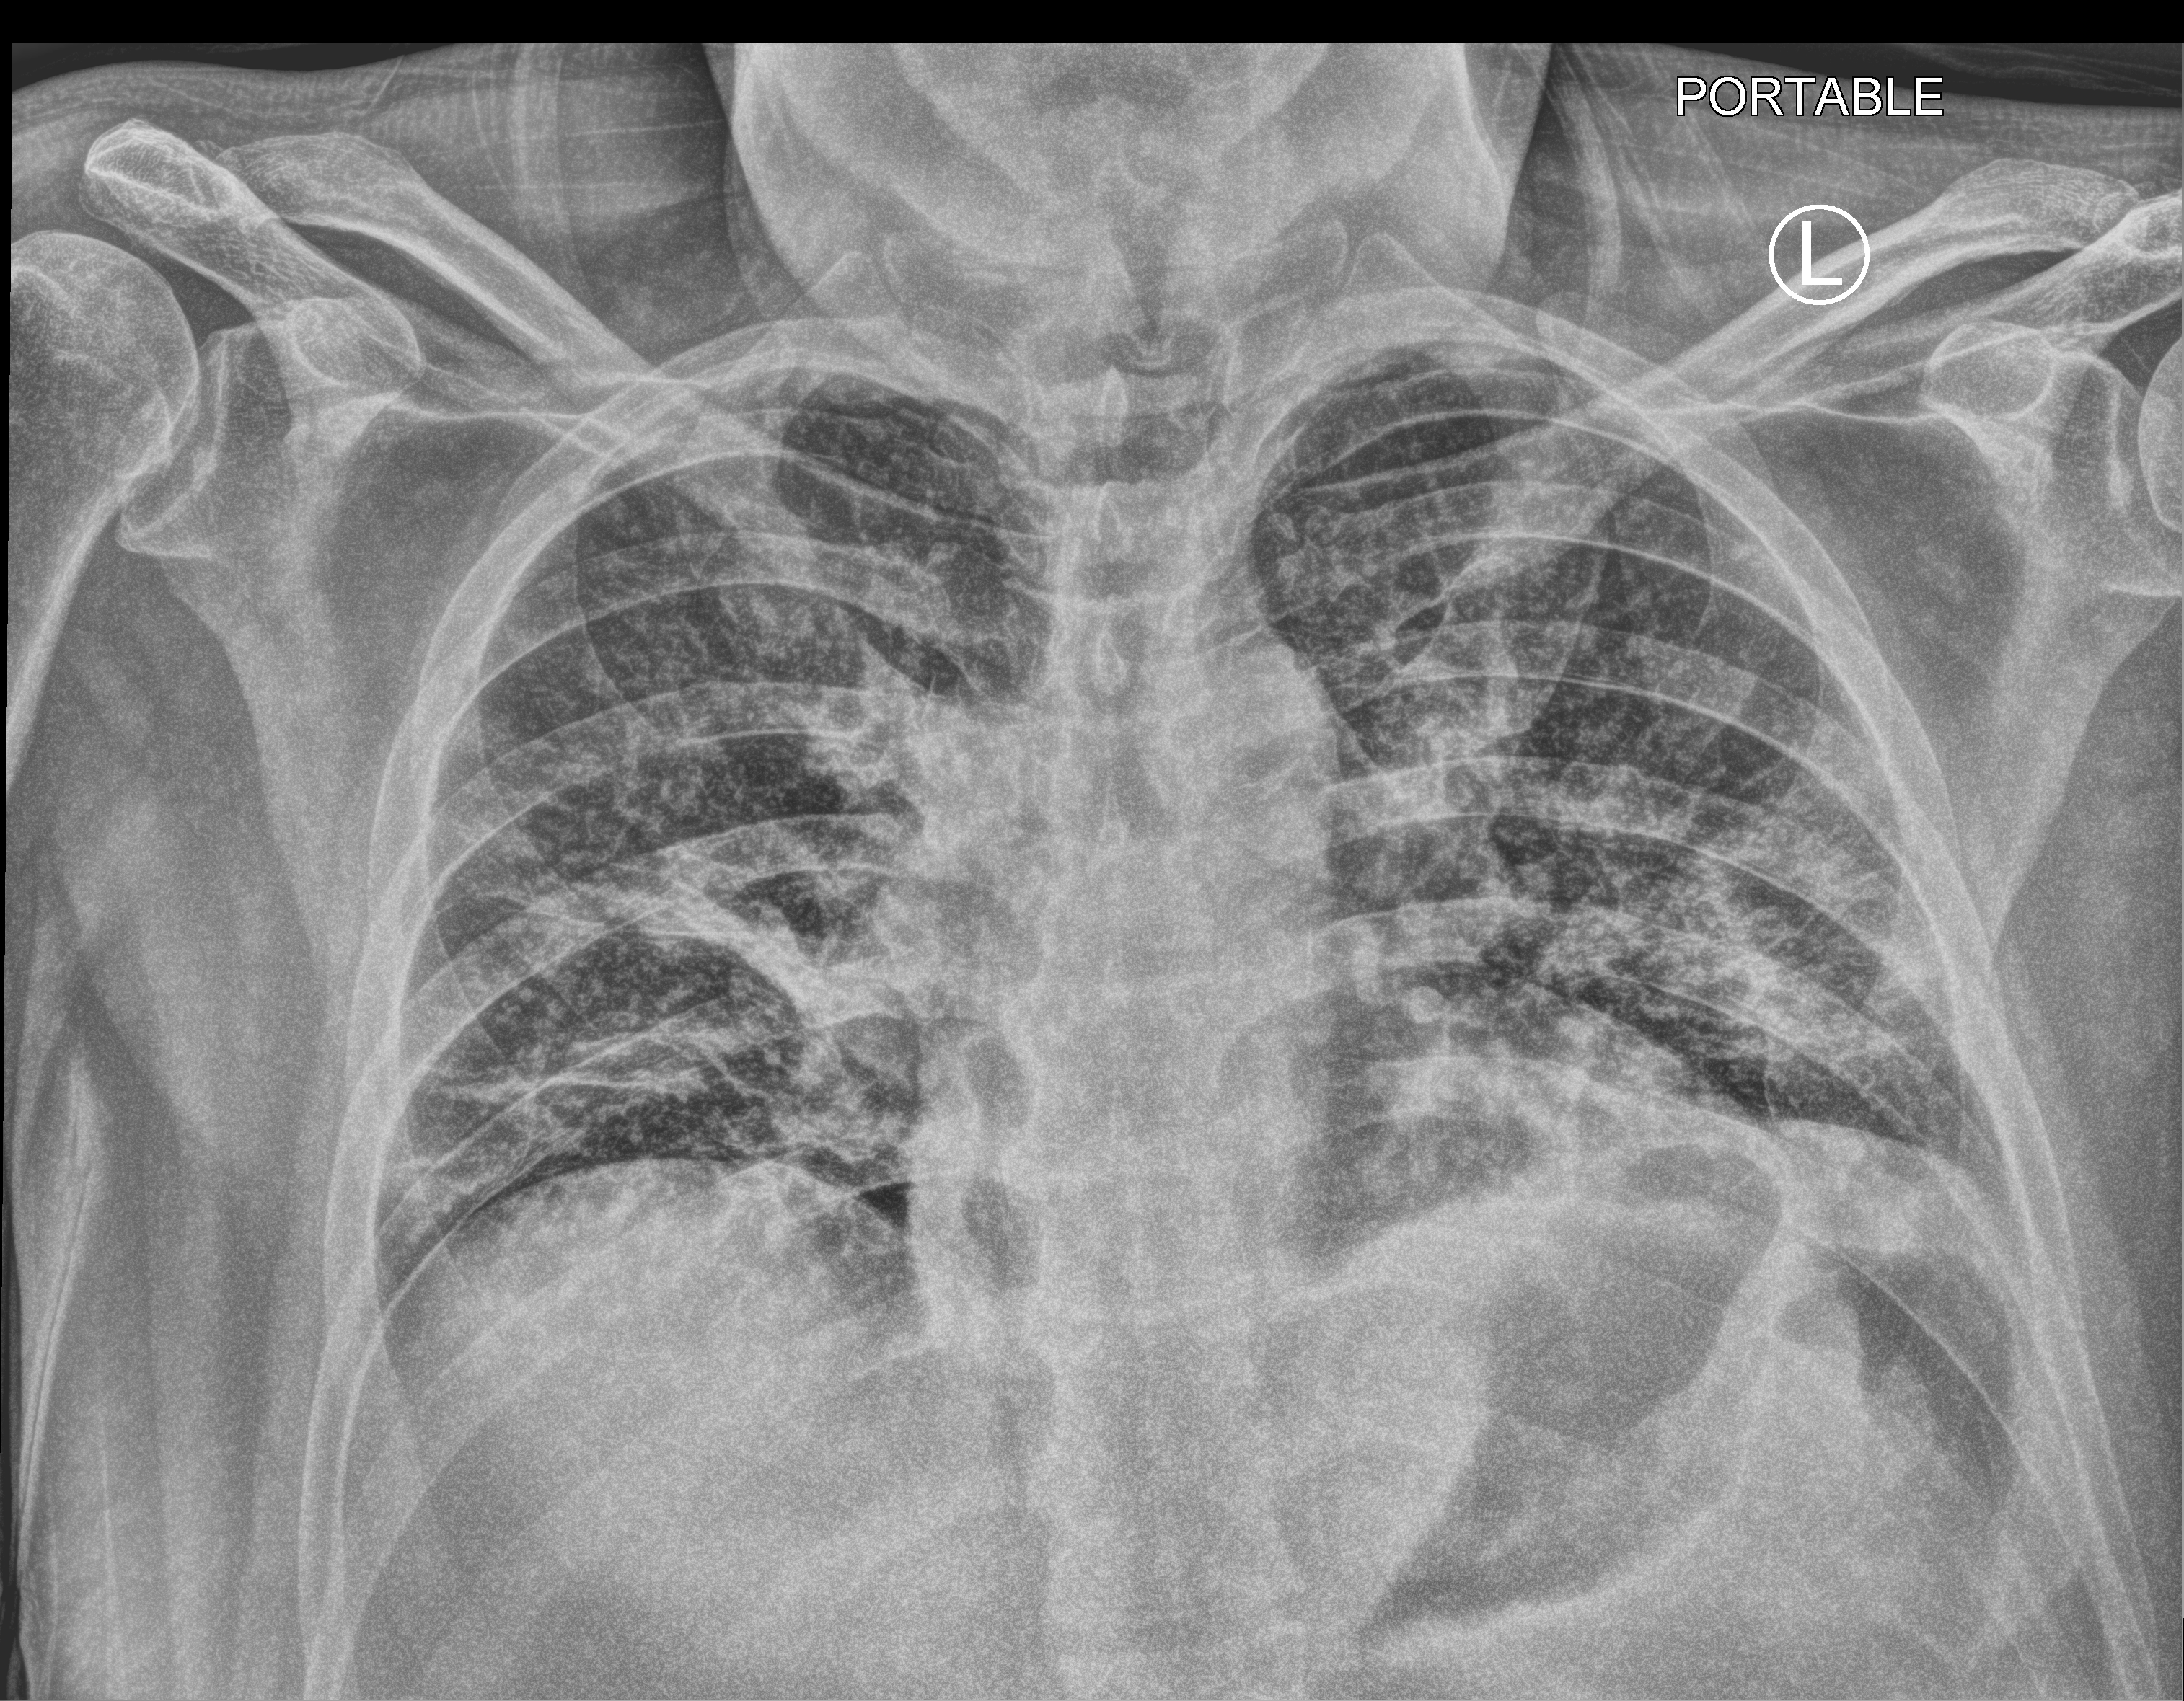
Bedside chest radiograph (computed radiography). Male patient hospitalised with COVID-19, age 60–74 years.
Admission-level facts for this patient (not findings on this image; timing relative to this image not recorded): mechanically ventilated during this hospital stay: no.